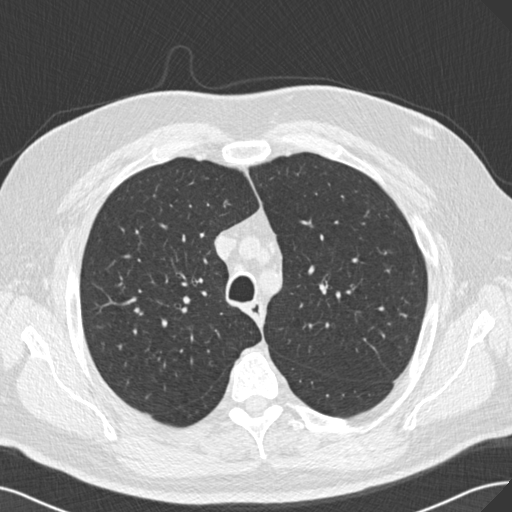
Axial slice from a low-dose chest CT screening exam. Baseline annual screen. Lung window (W 1500 / L -600 HU). Standard (soft-tissue) reconstruction kernel (B30f). Slice 44 of 175 in the series. Male, age 67 years at enrolment. Current smoker at enrolment.
Lesion marked by an expert reader, box from (x=130, y=303) to (x=147, y=322) px. Screening reader's record for this exam: no non-calcified nodule ≥4 mm recorded. Official screen result: negative screen, minor abnormalities not suspicious for lung cancer. Later outcome: lung cancer diagnosed 561 days after this screen (after the second annual screen) — small cell carcinoma, NOS, right middle lobe, stage IA (AJCC 6th edition), 20 mm at pathology.